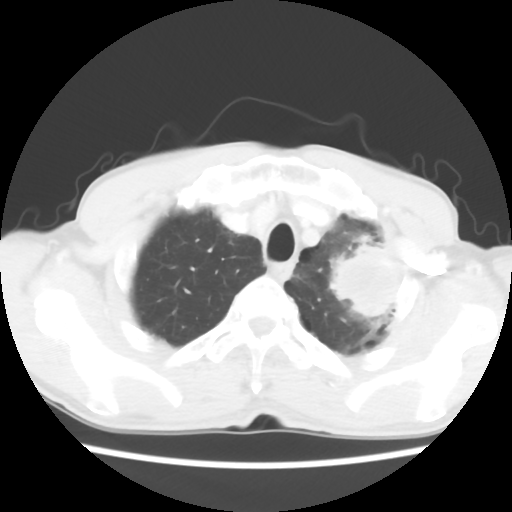
Chest CT, one axial slice; slice 51 of 60 in the series (ordered by position); reconstruction kernel STANDARD; 120 kVp; lung window (W 1500 / L -600 HU); 512 × 512 image matrix, field of view 308 × 308 mm. Male patient, age 64 years. From the clinical record (not read from this slice): clinical TNM (as recorded): T3 N3 M0; histopathological grade: G3.
Annotated regions visible in this slice (rectangle marked by the reading radiologist):
- lung tumour (recorded histology: adenocarcinoma): box from (x=319, y=235) to (x=401, y=332) px